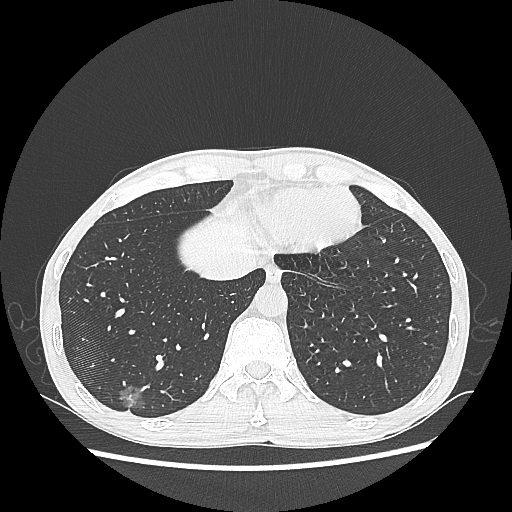
Chest CT, one axial slice; slice 68 of 270 in the series (ordered by position); lung window (W 1500 / L -600 HU); 1.25 mm slice thickness; 512 × 512 image matrix, field of view 360 × 360 mm. Male patient, age 60 years. Case-level facts recorded for this patient, not image findings: clinical TNM (as recorded): T1c N0 M0; histopathological grade: G2.
Annotated regions visible in this slice (bounding box drawn by a radiologist):
- lung tumour (recorded histology: adenocarcinoma): box from (x=113, y=380) to (x=149, y=411) px